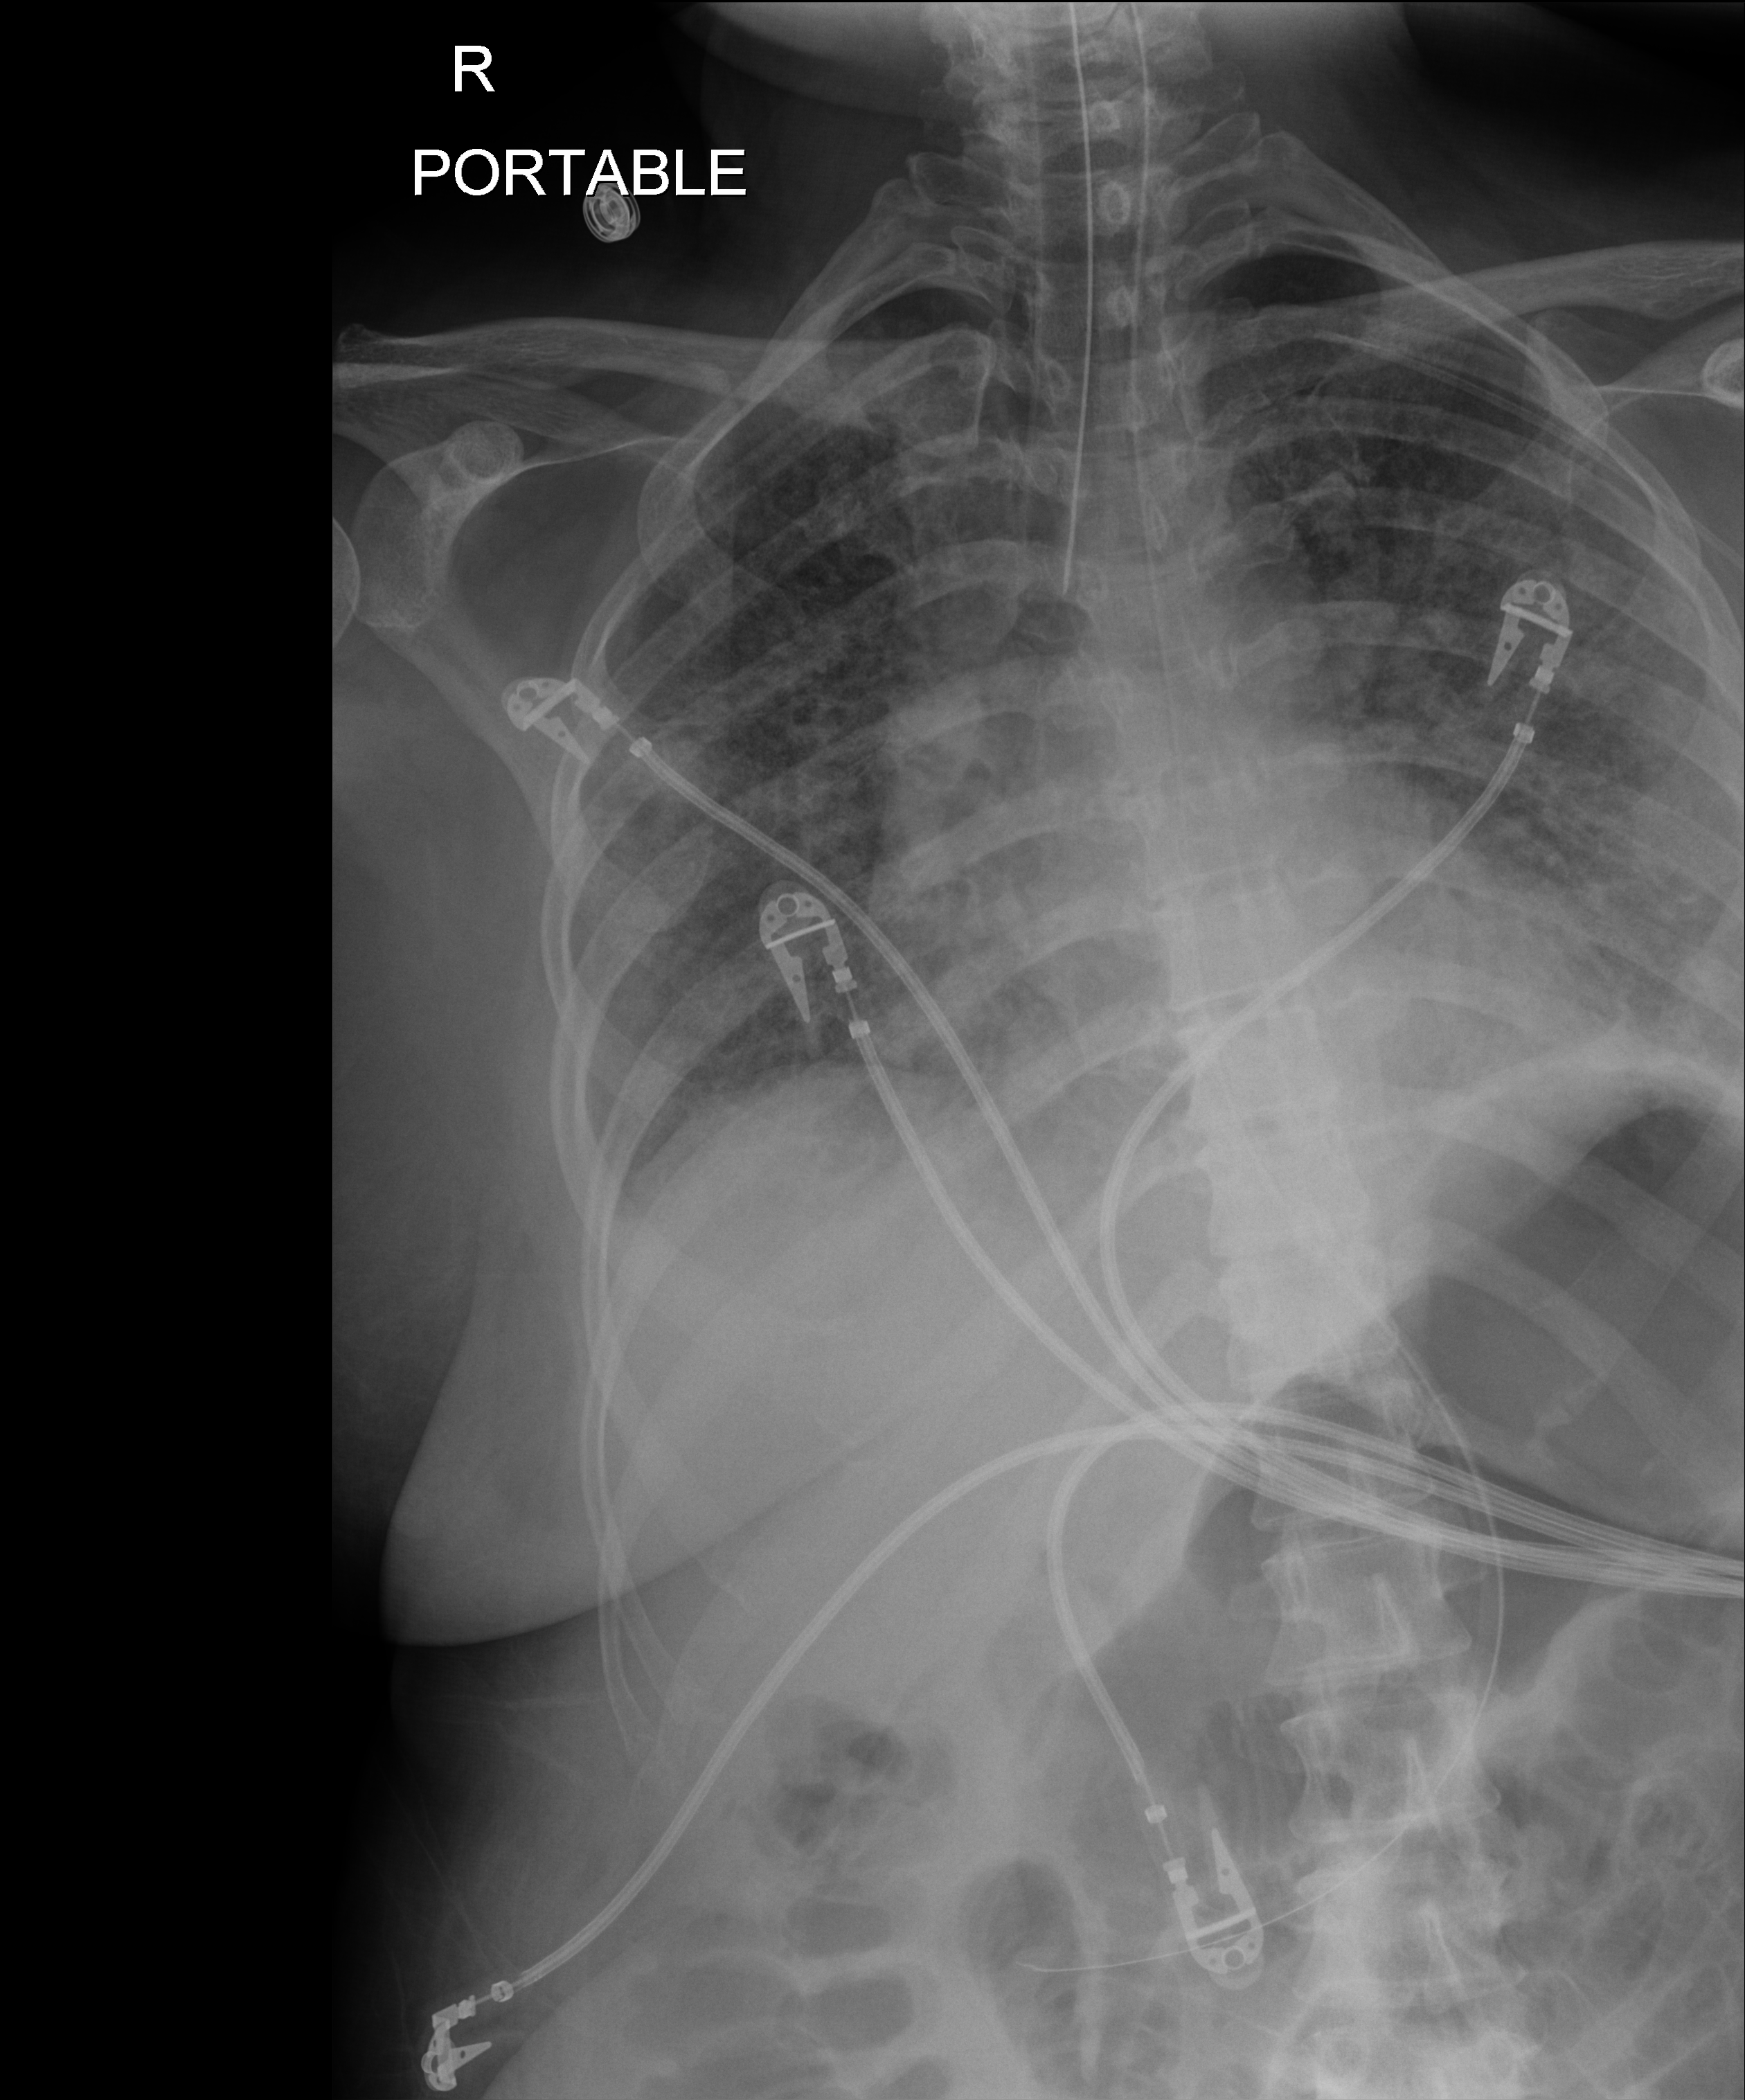
Bedside chest radiograph (digital radiography), anteroposterior (AP) projection. Patient hospitalised with COVID-19; male, aged 18–59 years.
From the hospital-stay record, not from the radiograph (when in the stay this image was taken is not recorded):
- admitted to intensive care during this hospital stay: yes
- other chronic lung disease (admission record): no
- length of hospital stay: 38 days